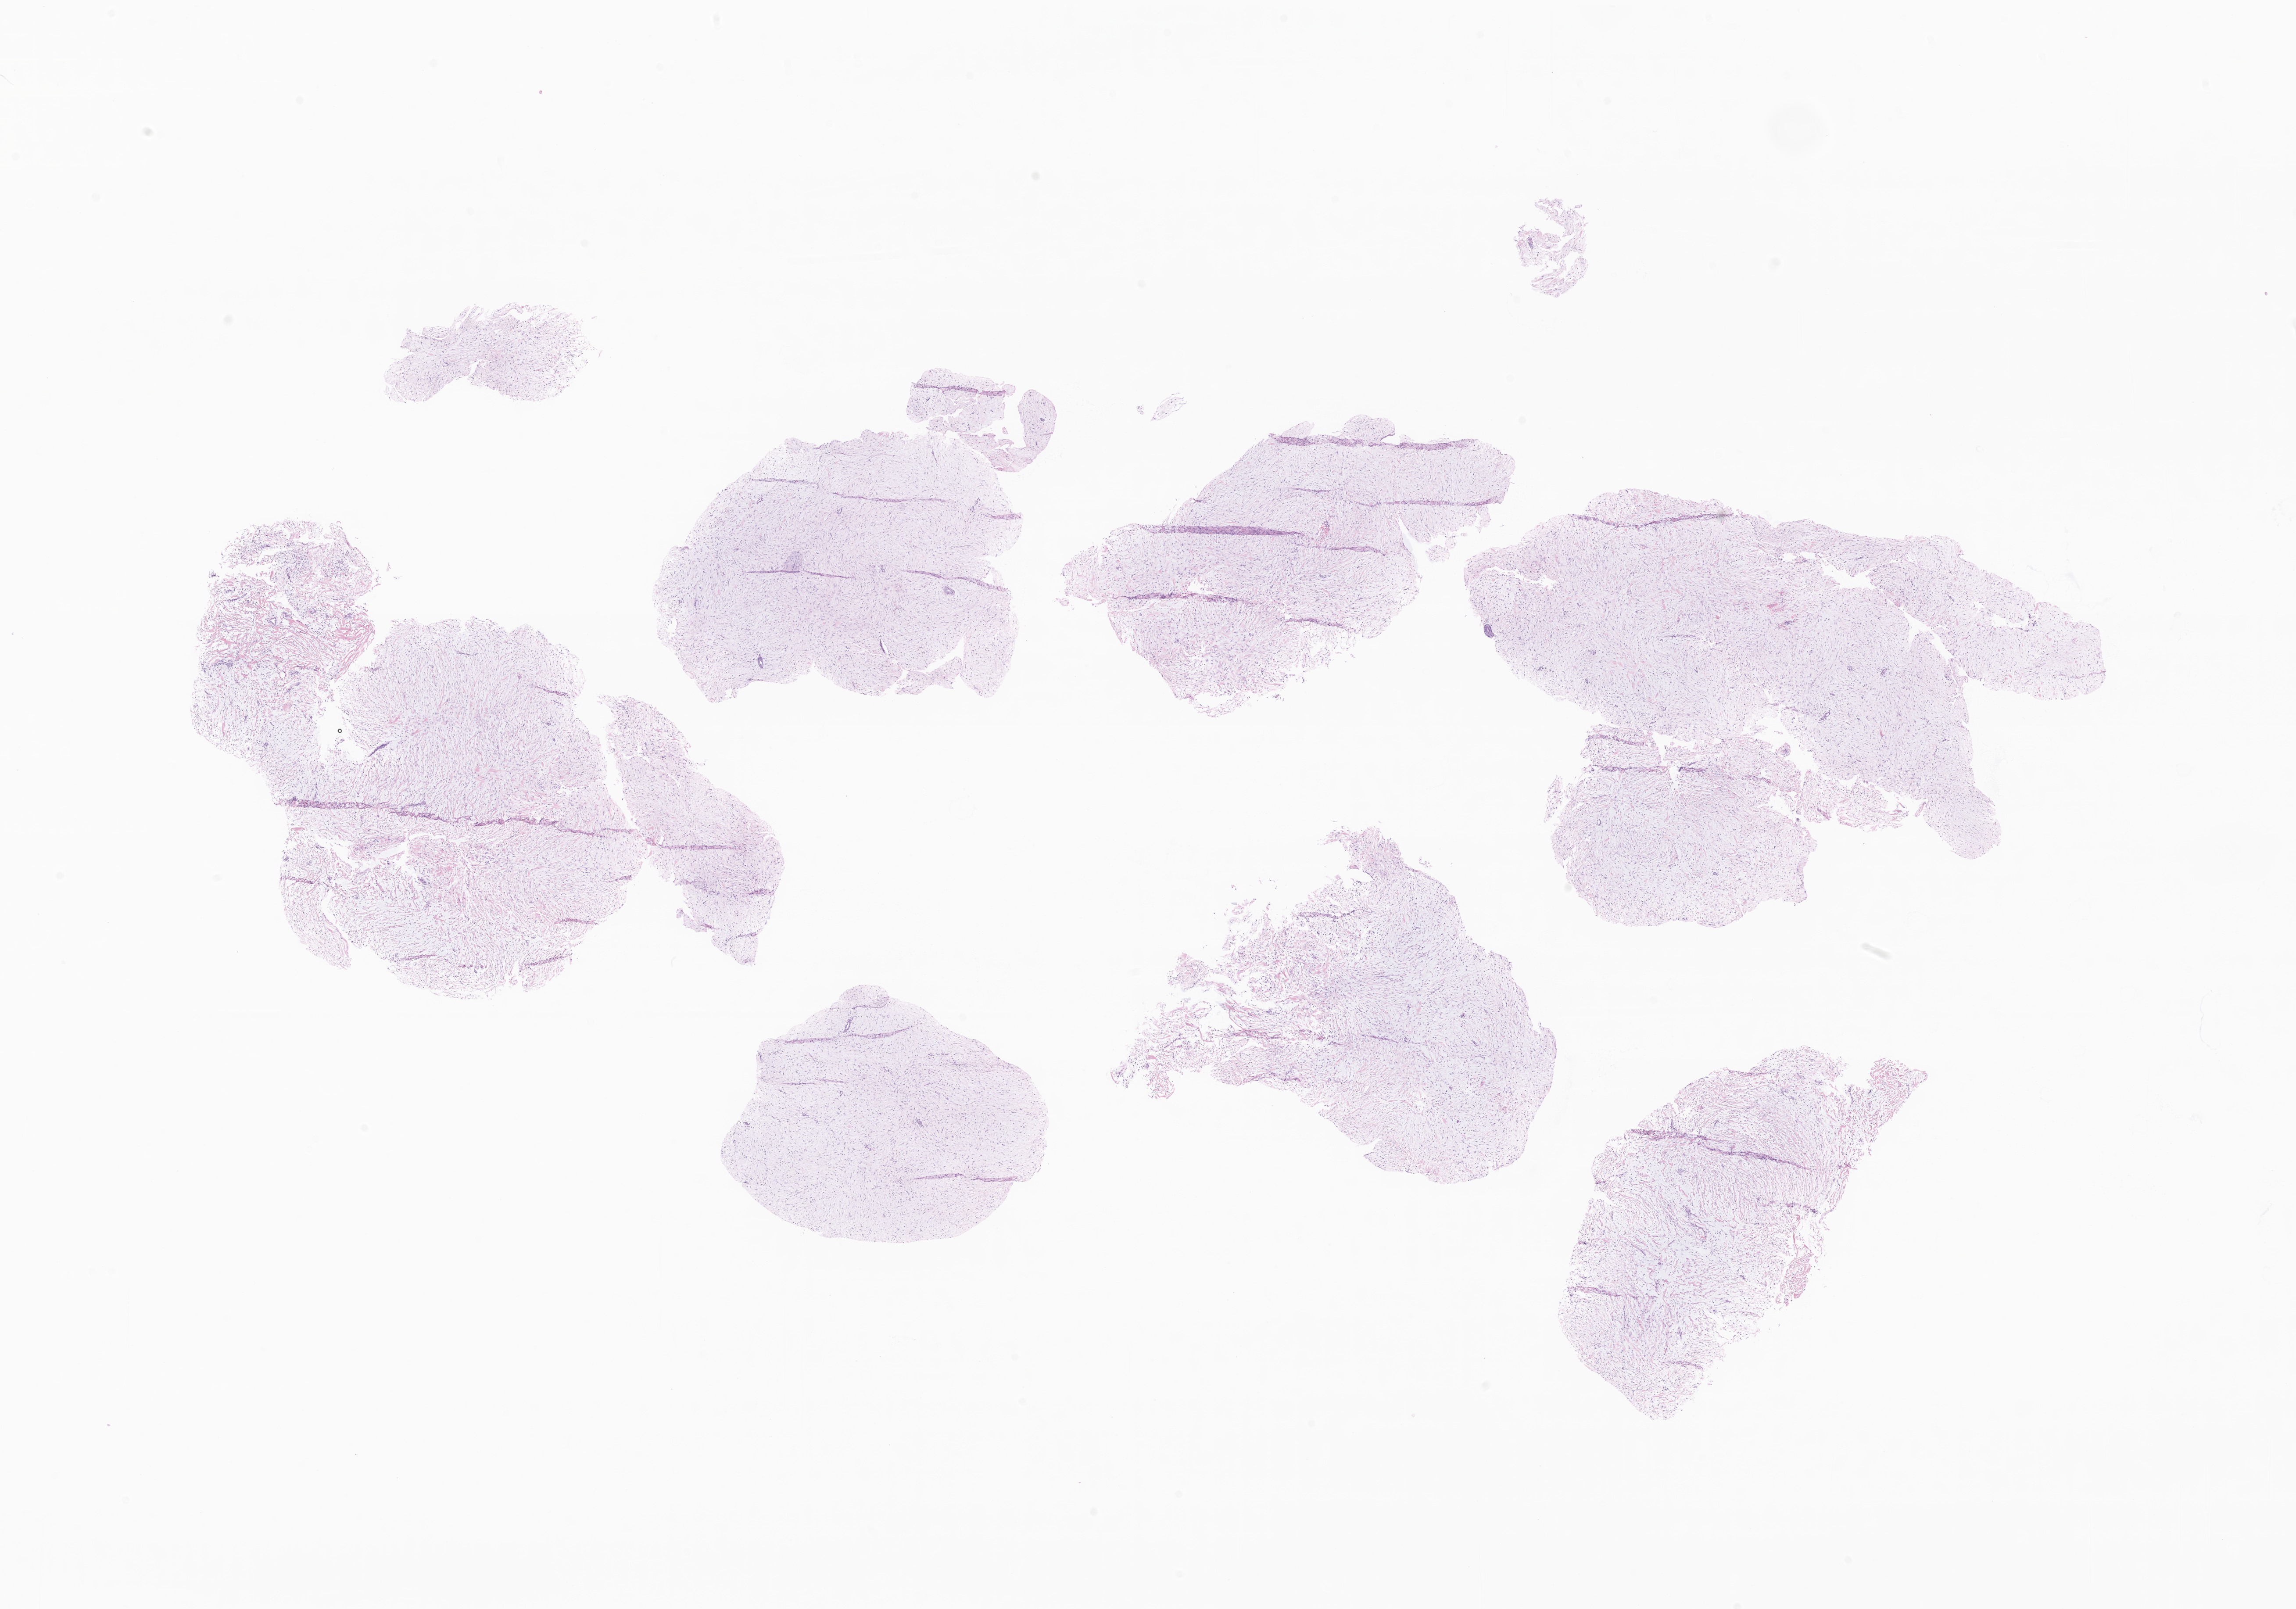
Digitized hematoxylin and eosin (H&E)-stained section of tumor tissue from the nasal cavity — low-resolution overview of the scanned area, about 22.1 x 15.5 mm; FFPE section. Male patient, age 711 days (about 1.9 years).
Recorded diagnosis: Aggressive fibromatosis.